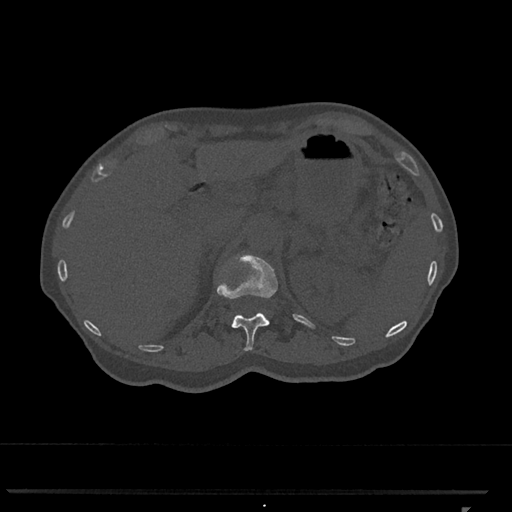
CT including the spine, one axial slice; slice 447 of 793 in the series (ordered by position); reconstruction kernel Br40s/3; bone window (W 1800 / L 400 HU); 0.5 mm slice thickness; 512 × 512 image matrix, field of view 380 × 380 mm. Patient: female, 62 years. From the clinical record (not read from this slice): primary cancer: renal.
Annotated regions visible in this slice (semi-automatically segmented with operator editing):
- T12 vertebra: bounding box (x1, y1, x2, y2) in pixels: (217, 254, 278, 351)